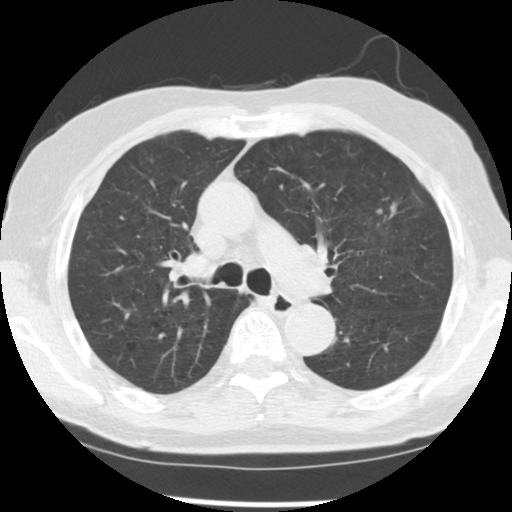
Low-dose screening chest CT, one axial slice; 140 kVp; lung window (W 1500 / L -600 HU); 512 × 512 image matrix.
Annotated regions visible in this slice (outlined manually by an expert reader):
- lesion 1 (tumor, upper lobe of left lung): bounding box [x1, y1, x2, y2] px = [376, 204, 397, 220]